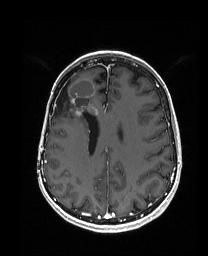
Brain MRI from a brain-tumour surgery series, one axial slice. Slice 68 of 192 in the series (ordered by position). T1-weighted post-contrast. 1 mm slice thickness. 208 × 256 image matrix, field of view 203 × 250 mm. Case-level facts recorded for this patient, not image findings: histopathology: Metastatic Carcinoma from Breast primary; tumour location: Right Frontal.
Annotated regions visible in this slice (manually delineated by an expert):
- previous resection cavity: box from (x=53, y=81) to (x=70, y=115) px
- tumour: (x=55, y=77)–(x=104, y=117)